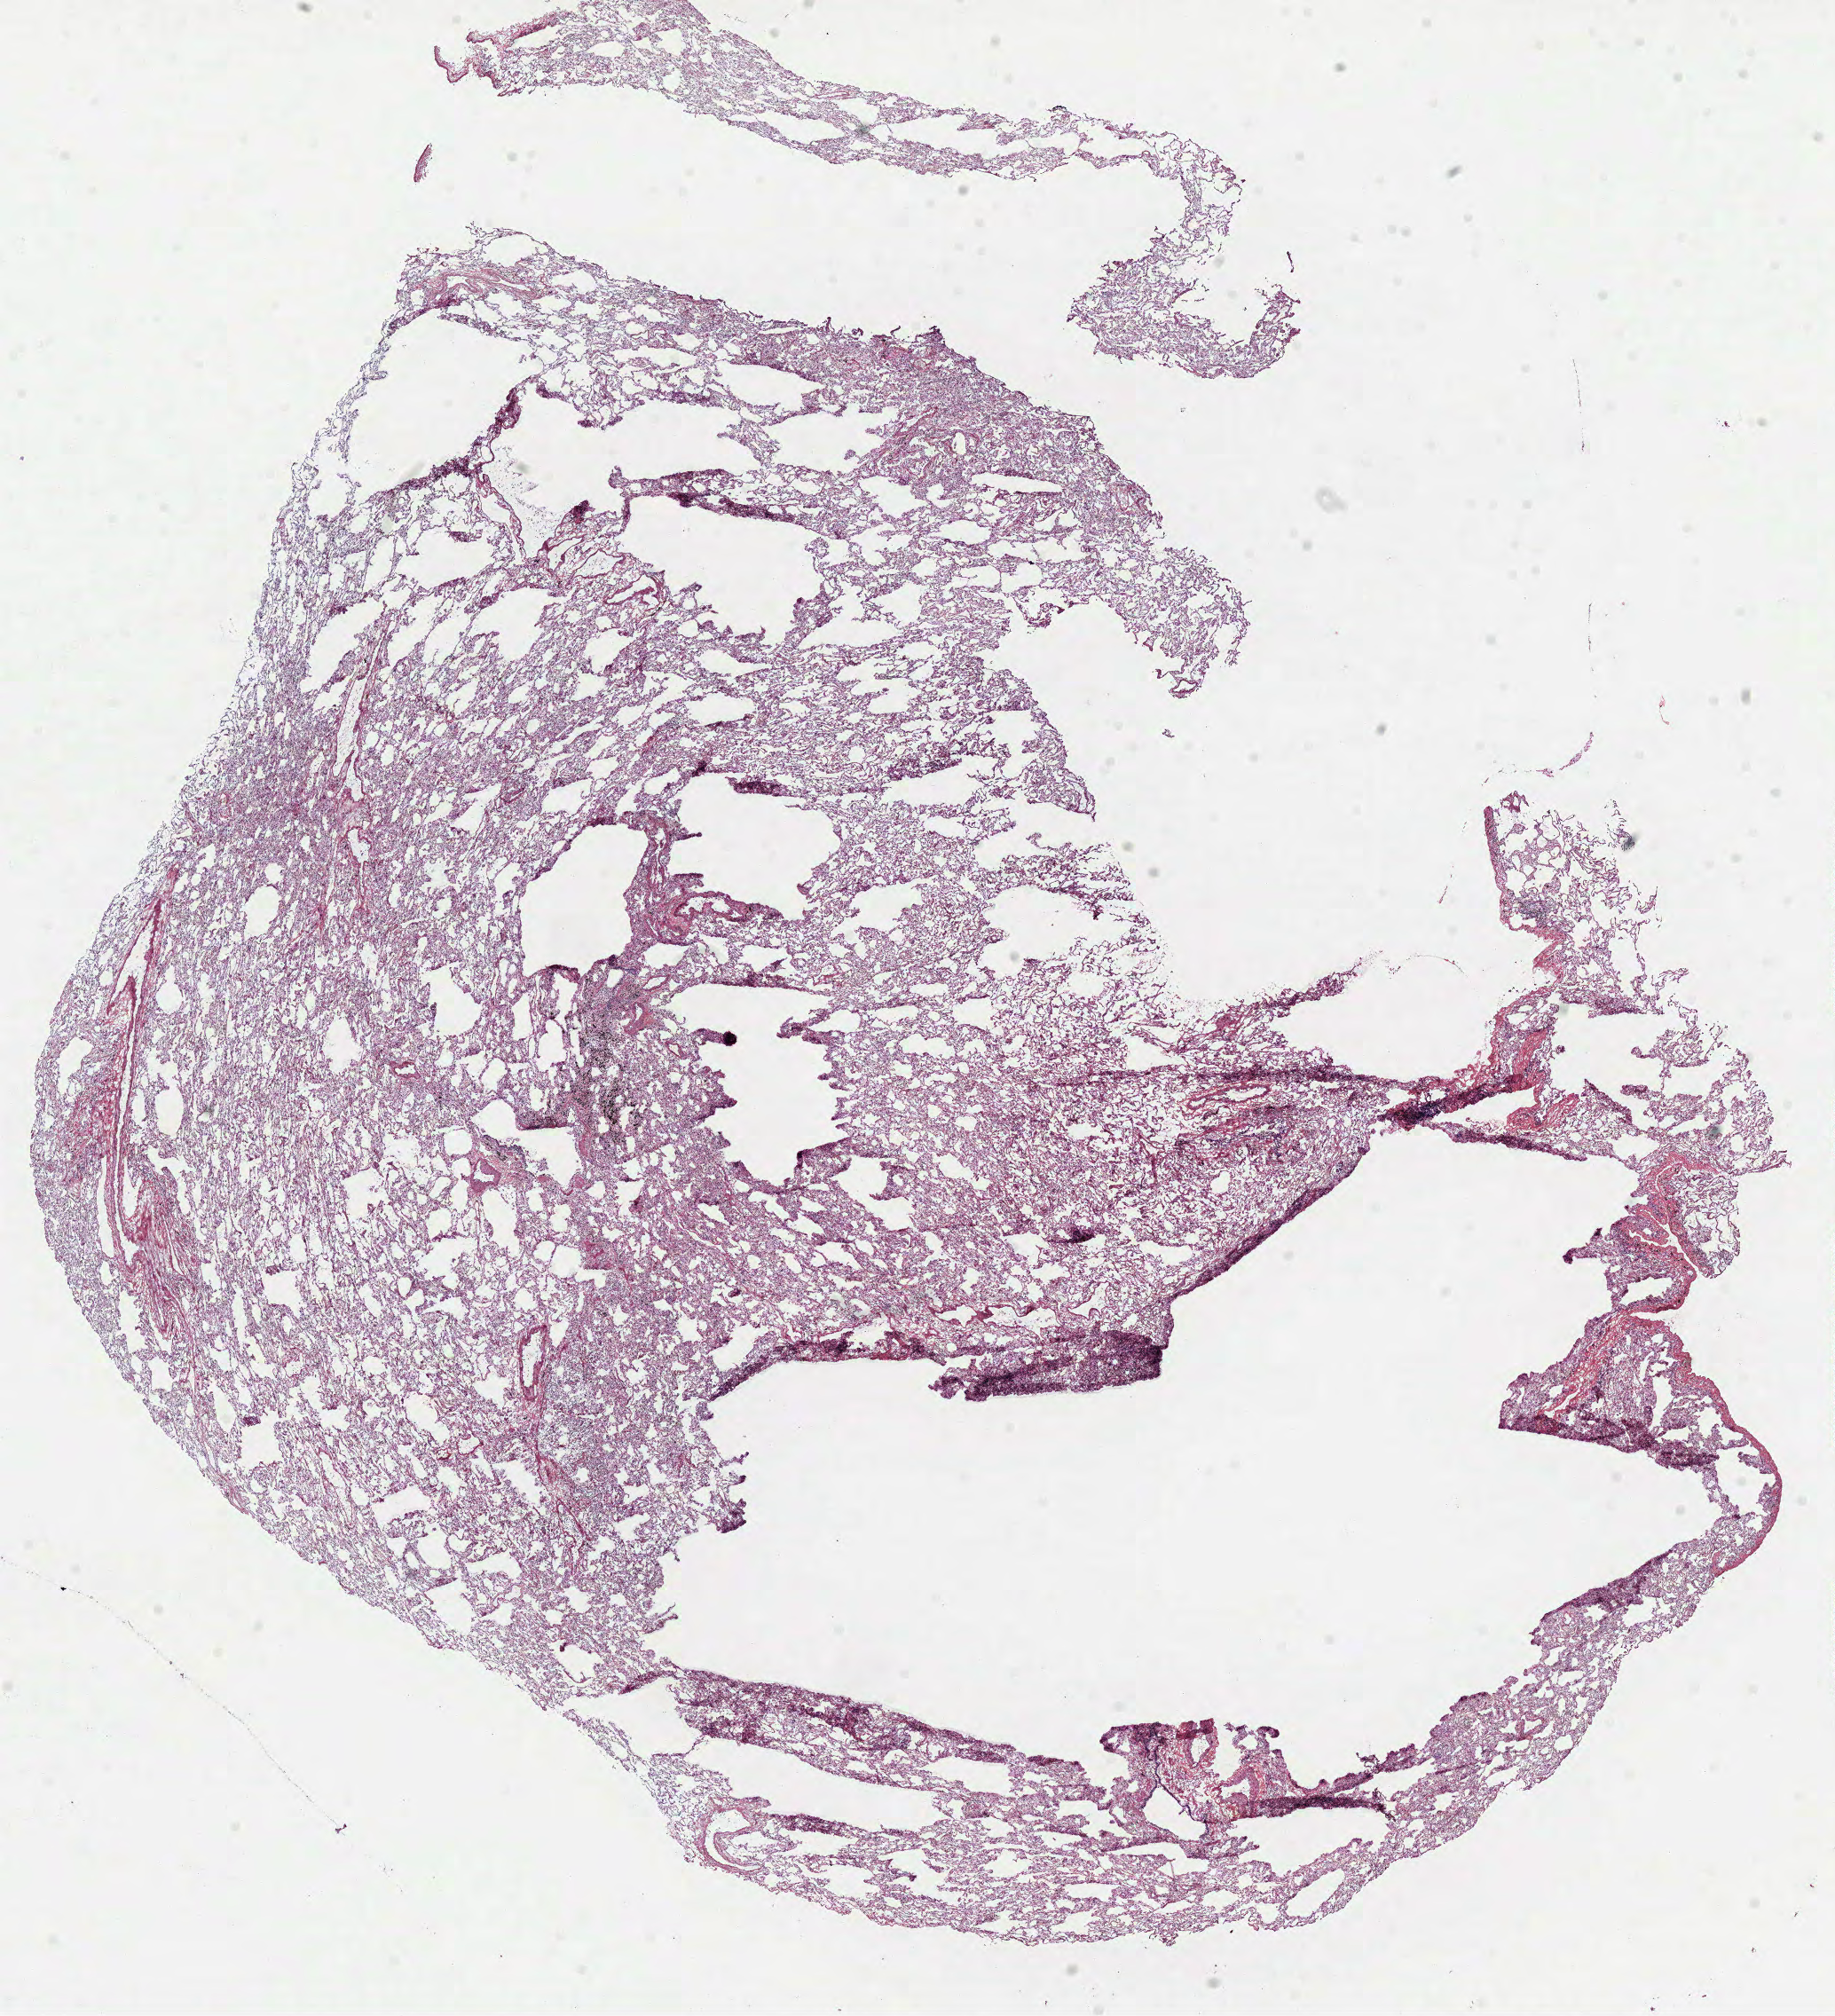
H&E whole-slide image — shown as a low-resolution overview of the whole scanned area (about 16.7 x 18.3 mm, slide scanned at 40x). Frozen section. Lung, solid tissue normal (non-tumour tissue) sample. Patient: female, age at initial diagnosis 45 years.
This section: solid tissue normal sample (biorepository sample class). Patient diagnosis: Squamous cell carcinoma, NOS (upper lobe, lung).